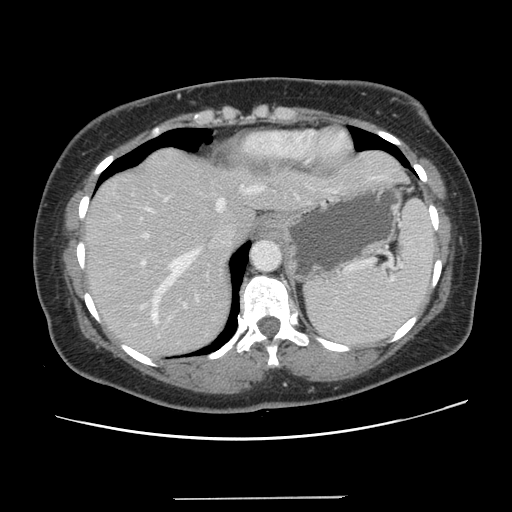
Contrast-enhanced abdominal CT, one axial slice; slice 105 of 141 in the series (ordered by position); 120 kVp; soft-tissue window (W 400 / L 40 HU); 2.5 mm slice thickness; 512 × 512 image matrix. Female patient, age 53 years. Case-level facts recorded for this patient, not image findings: diagnosis: colorectal cancer liver metastases, imaged before liver resection; multiple liver metastases: no; largest metastasis: 14.5 cm; disease in both lobes: yes.
Annotated regions visible in this slice (expert manual segmentation):
- hepatic veins: bounding box <114,182,267,324> (left, top, right, bottom; pixels)
- liver: <85,148,405,359>
- planned liver remnant (the part of the liver to remain after resection): <85,208,257,358>
- portal vein (with intrahepatic branches): <117,197,187,322>